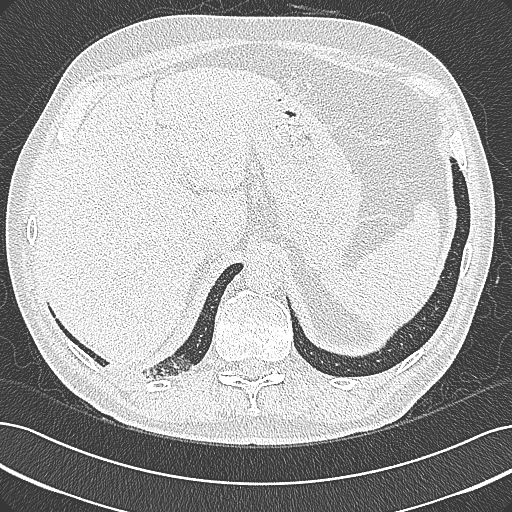
Axial slice from a low-dose chest CT screening exam. Baseline annual screen. Lung window (W 1500 / L -600 HU). Lung (sharp) reconstruction kernel (B80f). 512 × 512 image matrix, field of view 362 × 362 mm. Male participant, aged 68 years at enrolment. Former smoker at enrolment.
- Lesion marked by an expert reader, bounding box (x1, y1, x2, y2) in pixels: (92, 334, 200, 395).
- No non-calcified nodule or mass ≥4 mm was recorded by the screening reader at this exam.